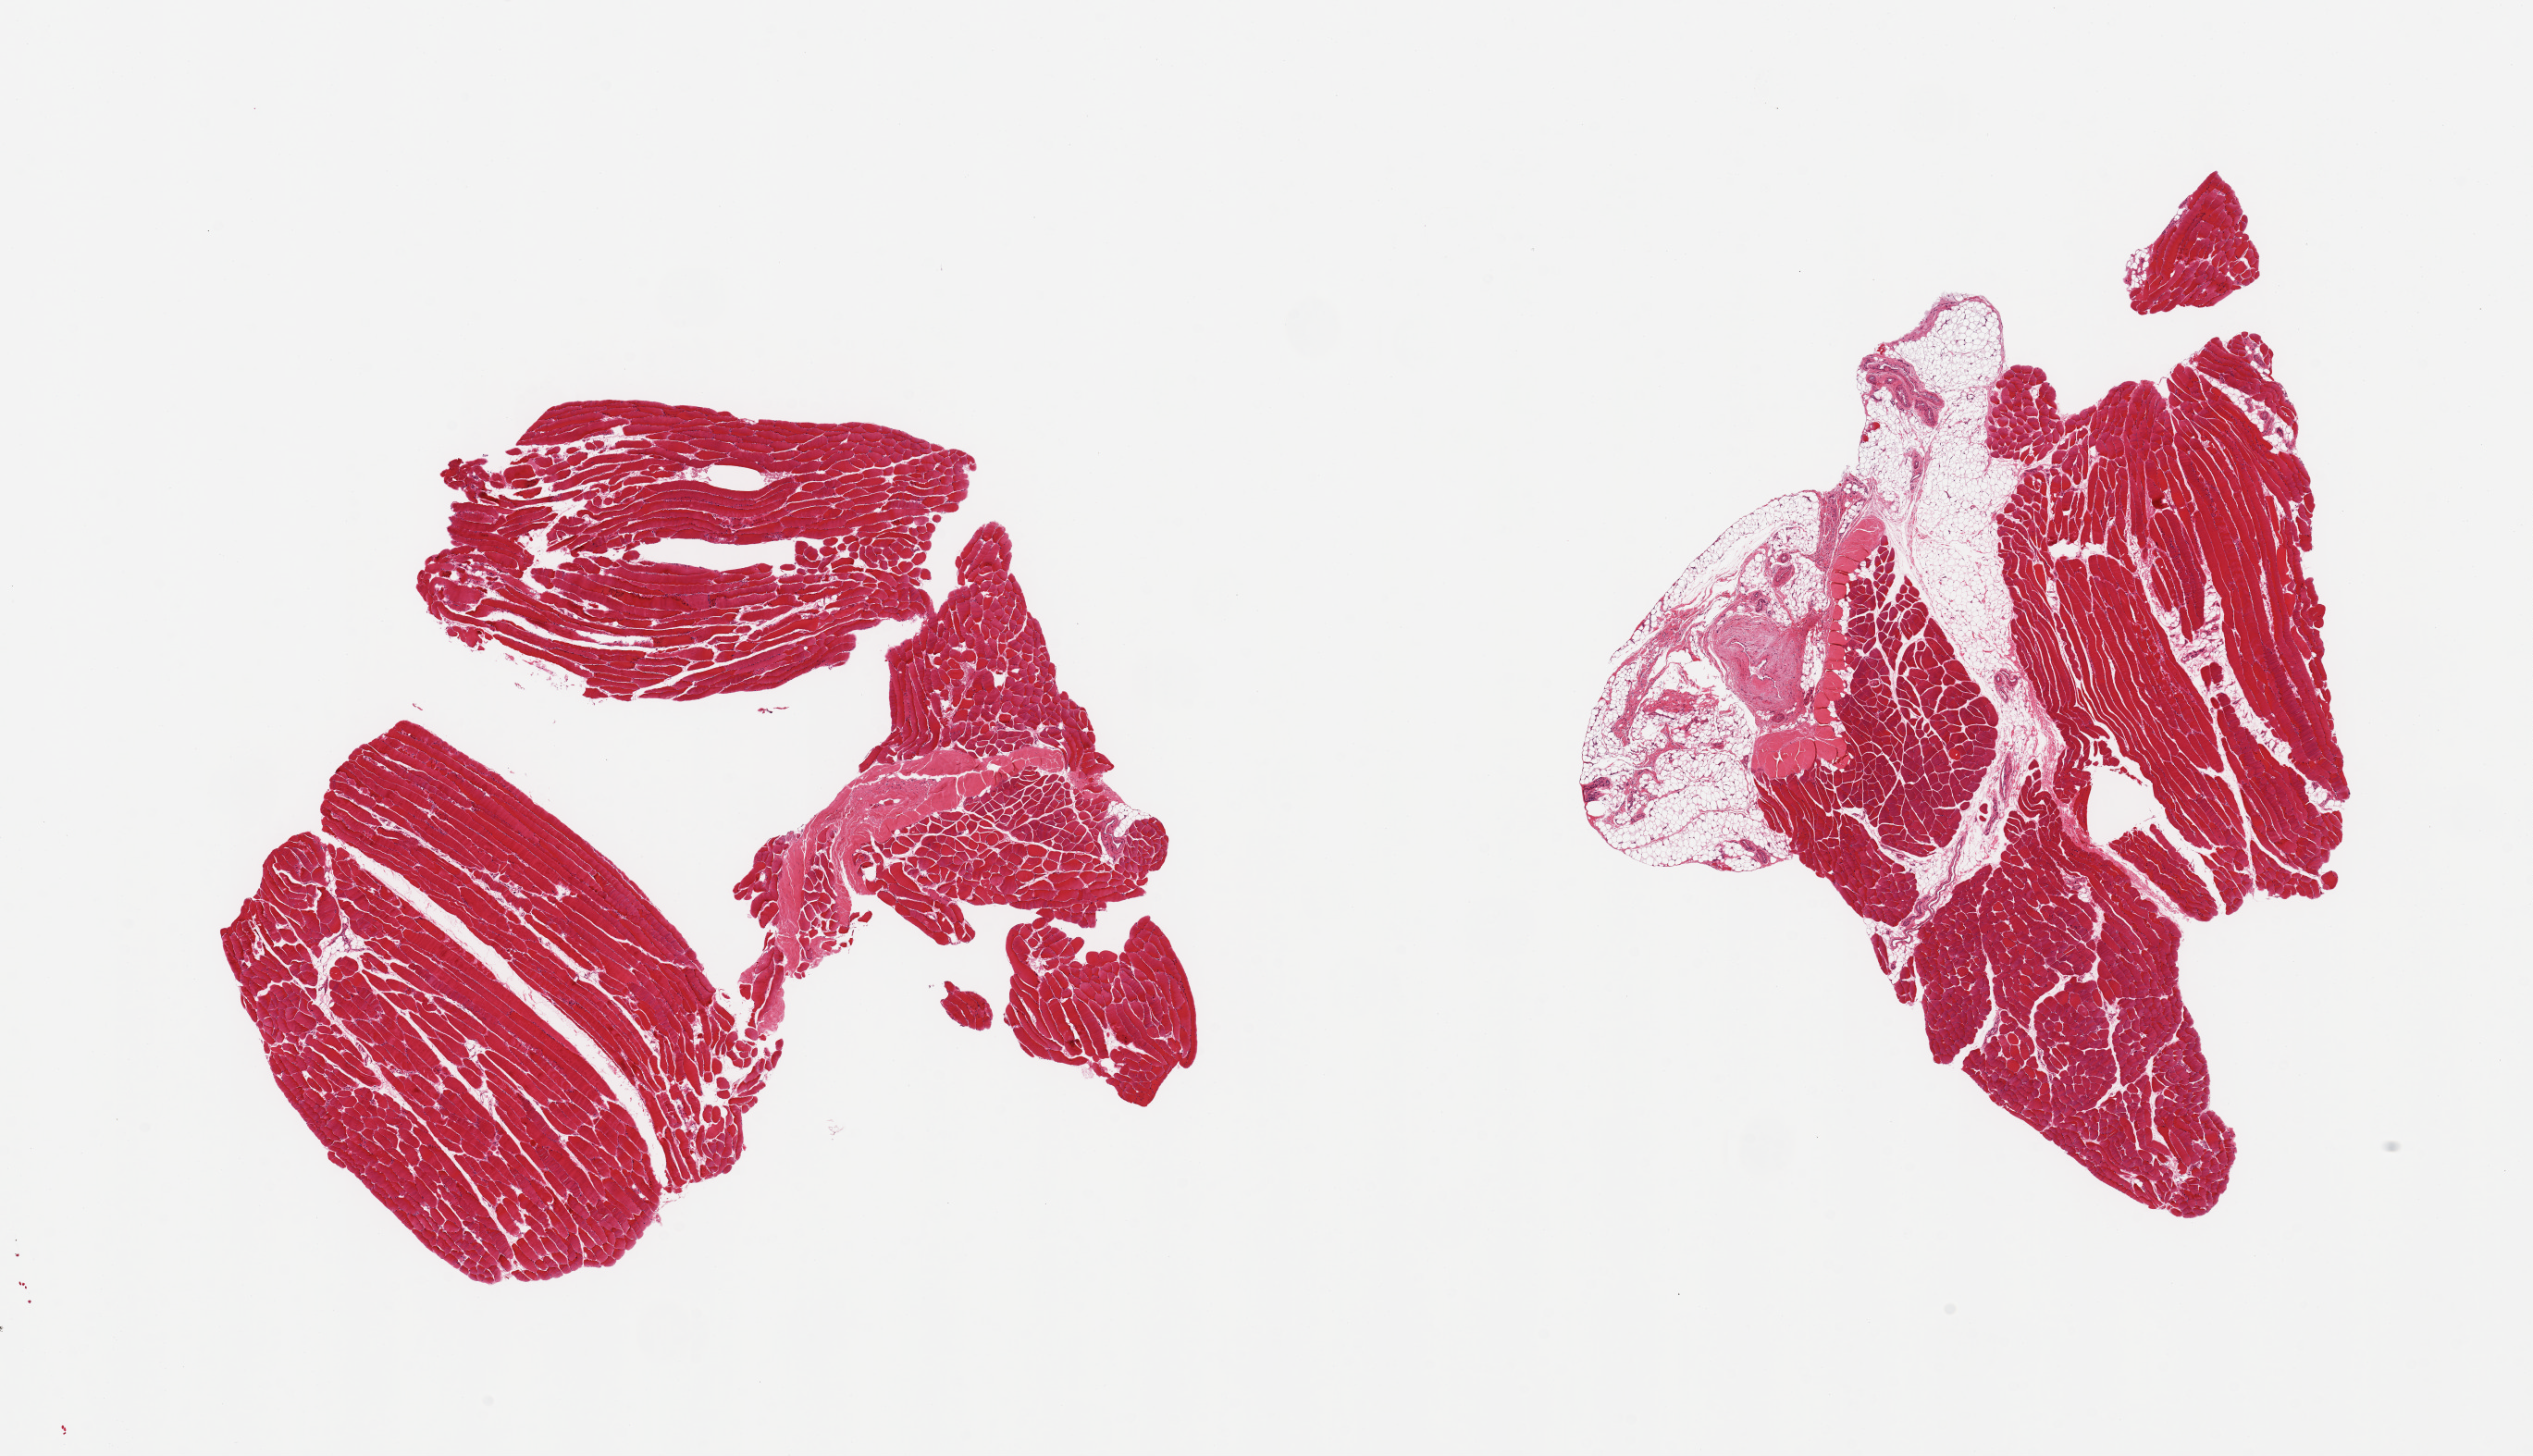
Whole-slide image, H&E stain, shown as a low-resolution overview of the whole scanned area (about 21.7 x 12.5 mm), PAXgene-fixed, paraffin-embedded tissue, section of skeletal muscle (target tissue), tissue donor sample. Donor sex: female.
Pathologist's review note for this sample: 2 pieces; 10% tendon in 1, 30% fibrofatty and tendon in other.